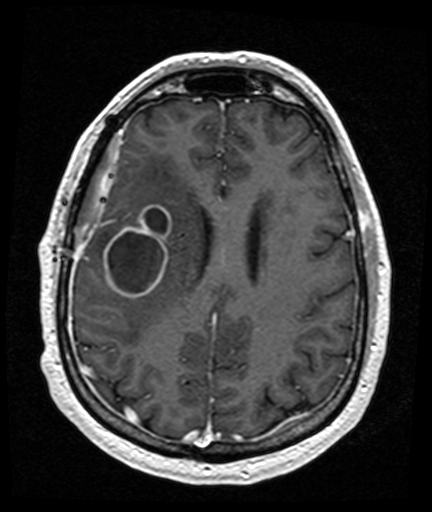
Brain MRI from a brain-tumour surgery series, one axial slice. Slice 58 of 176 in the series (ordered by position). T1-weighted post-contrast. 432 × 512 image matrix, field of view 194 × 230 mm. Case-level facts recorded for this patient, not image findings: histopathology: Glioblastoma; WHO grade: 4.
Outlined on this slice (outlined manually by an expert reader):
- tumour: bounding box <104,206,172,299> (left, top, right, bottom; pixels)